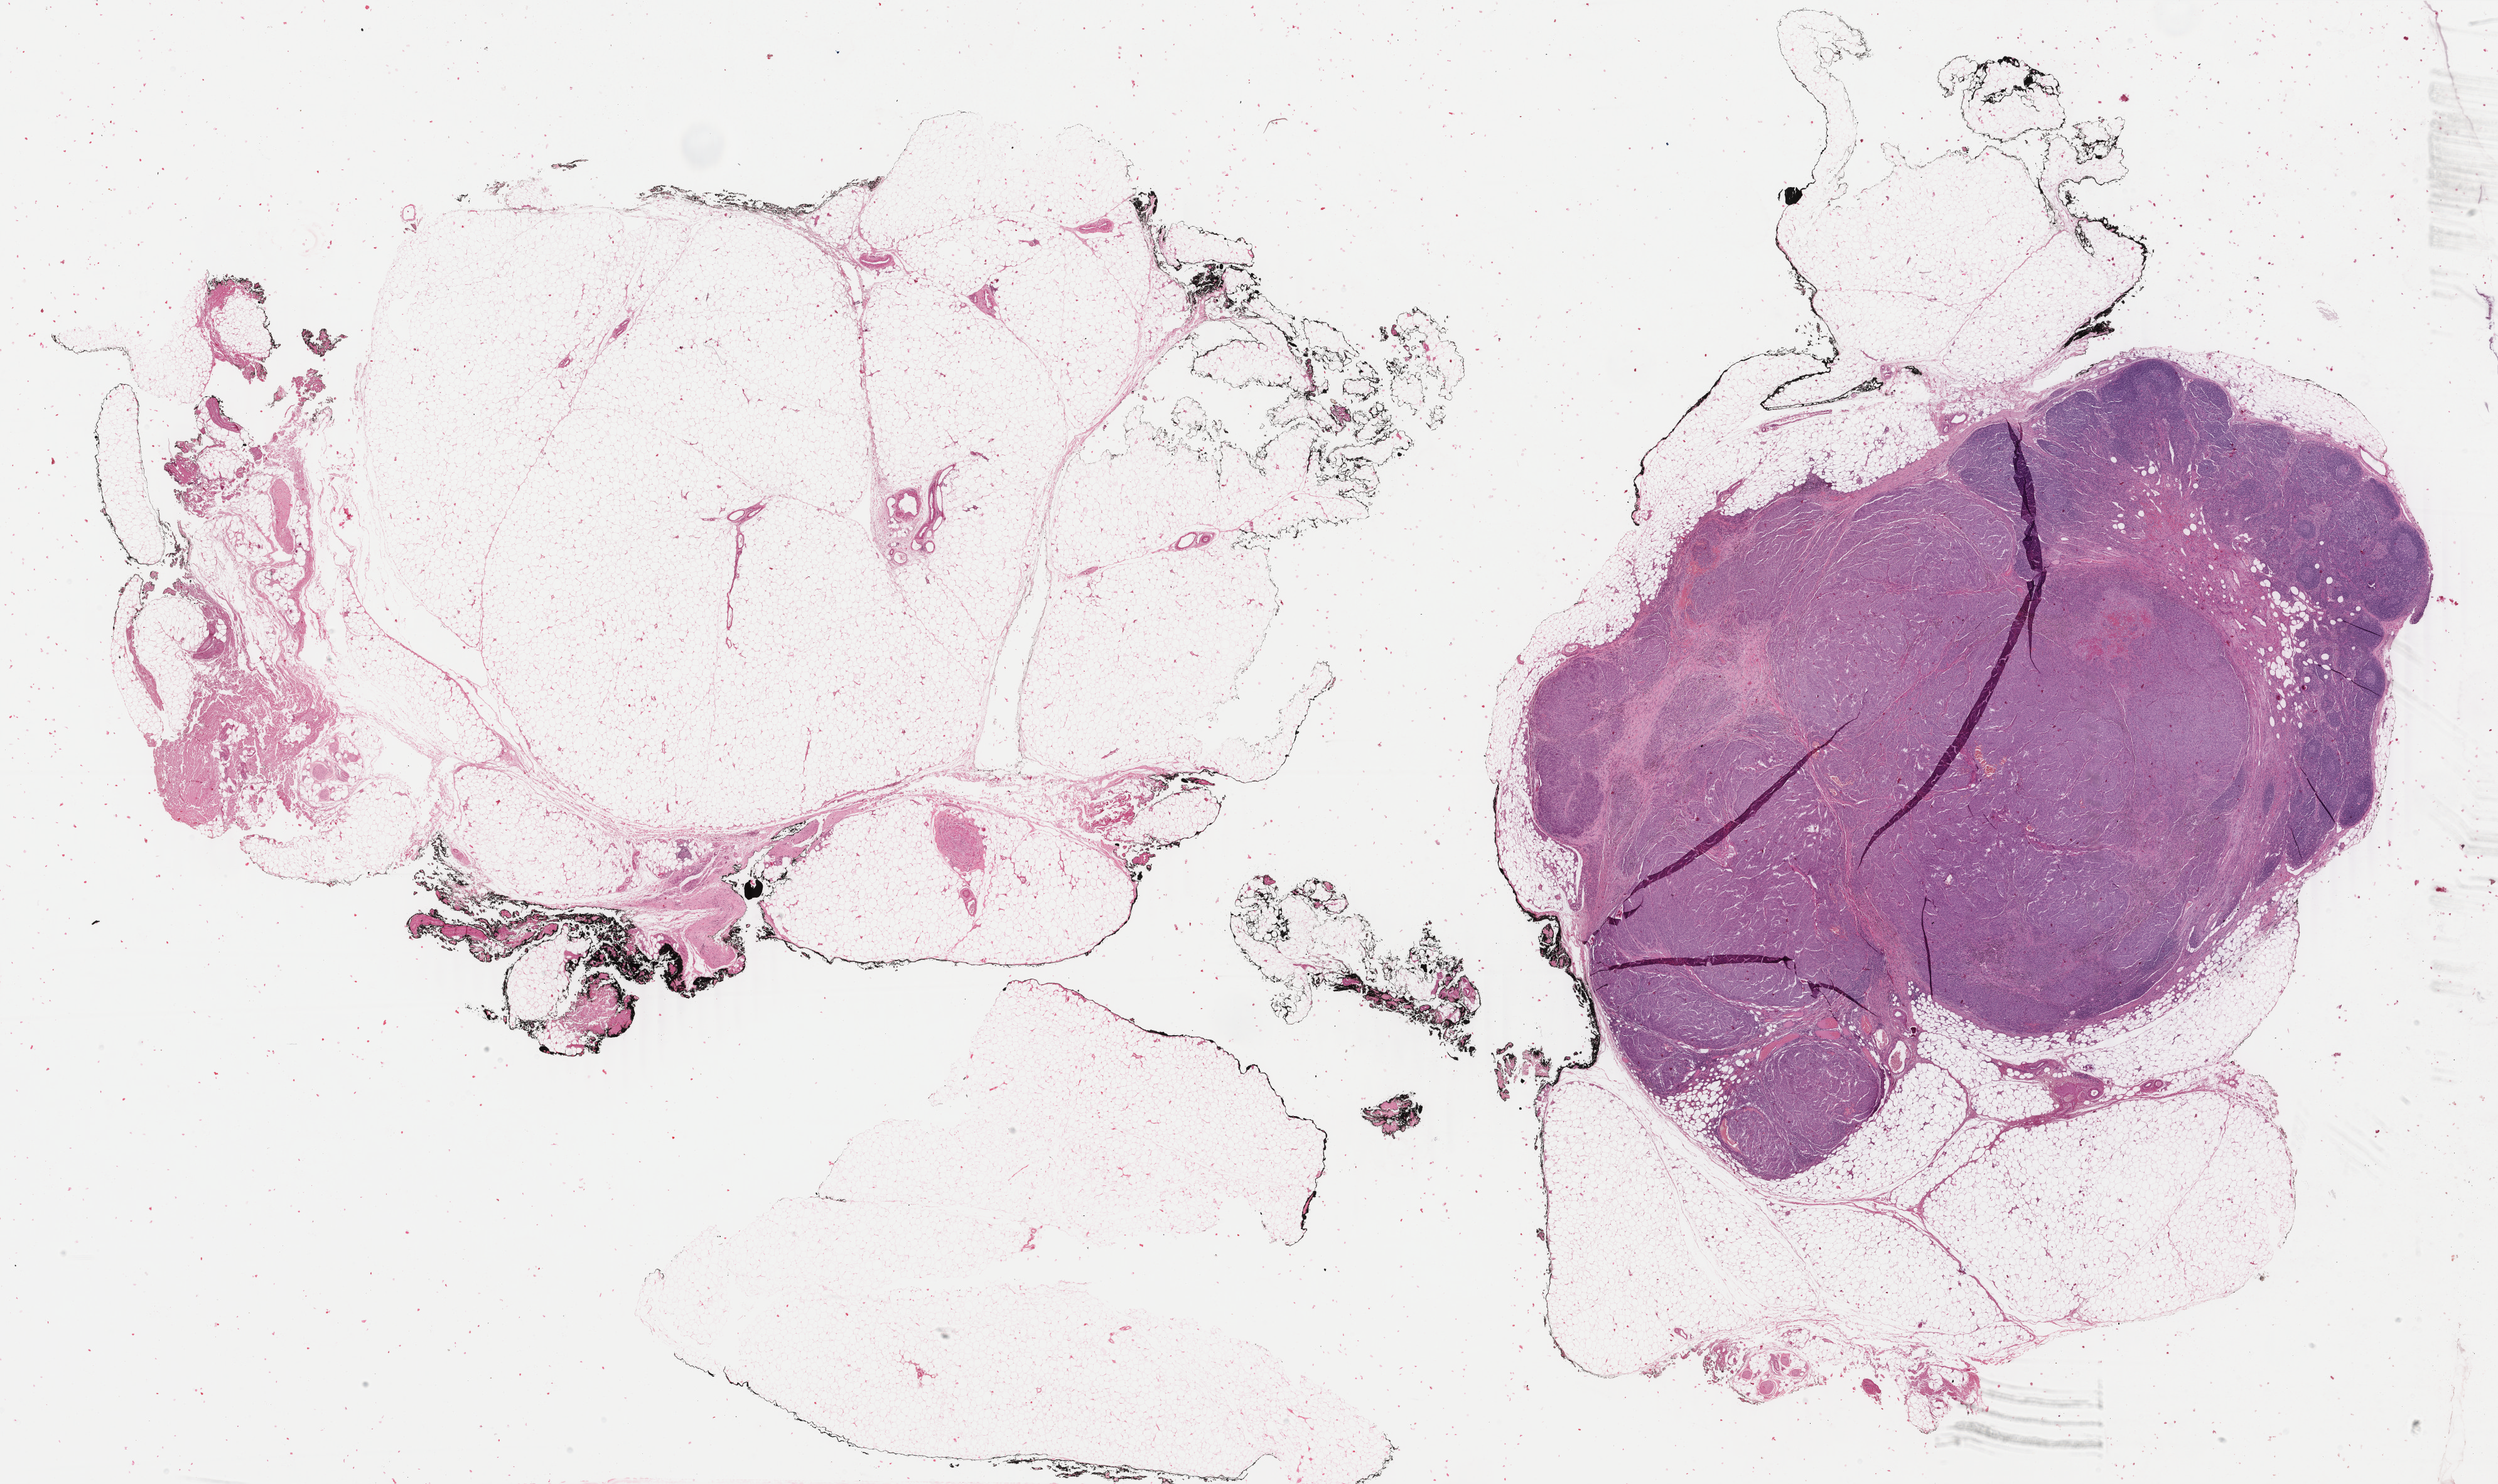
H&E whole-slide image — shown as a low-resolution overview of the whole scanned area (about 31.6 x 18.8 mm, acquisition: 40x scan), formalin-fixed paraffin-embedded (FFPE) diagnostic section, sample: primary tumour, skin. Patient: male, age at initial diagnosis 46 years.
* diagnosis: Malignant melanoma, NOS